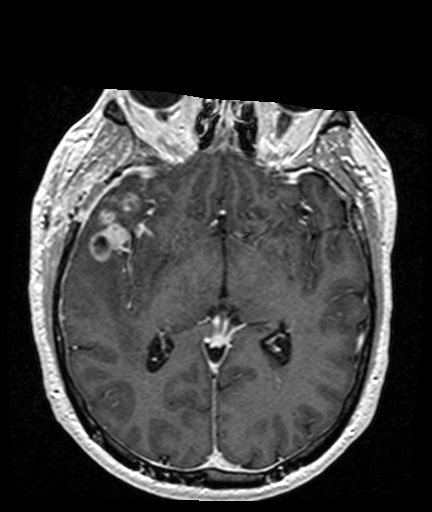
Brain MRI from a brain-tumour surgery series, one axial slice; T1-weighted post-contrast; 1 mm slice thickness; 432 × 512 image matrix, field of view 194 × 230 mm. From the clinical record (not read from this slice): histopathology: Glioblastoma; WHO grade: 4; IDH mutation: no; tumour location: Right Frontal Temporal, Posterior Sylvian Fissure.
Structures marked on this image (manually delineated by an expert):
- tumour: bounding box <89,191,146,262> (left, top, right, bottom; pixels)